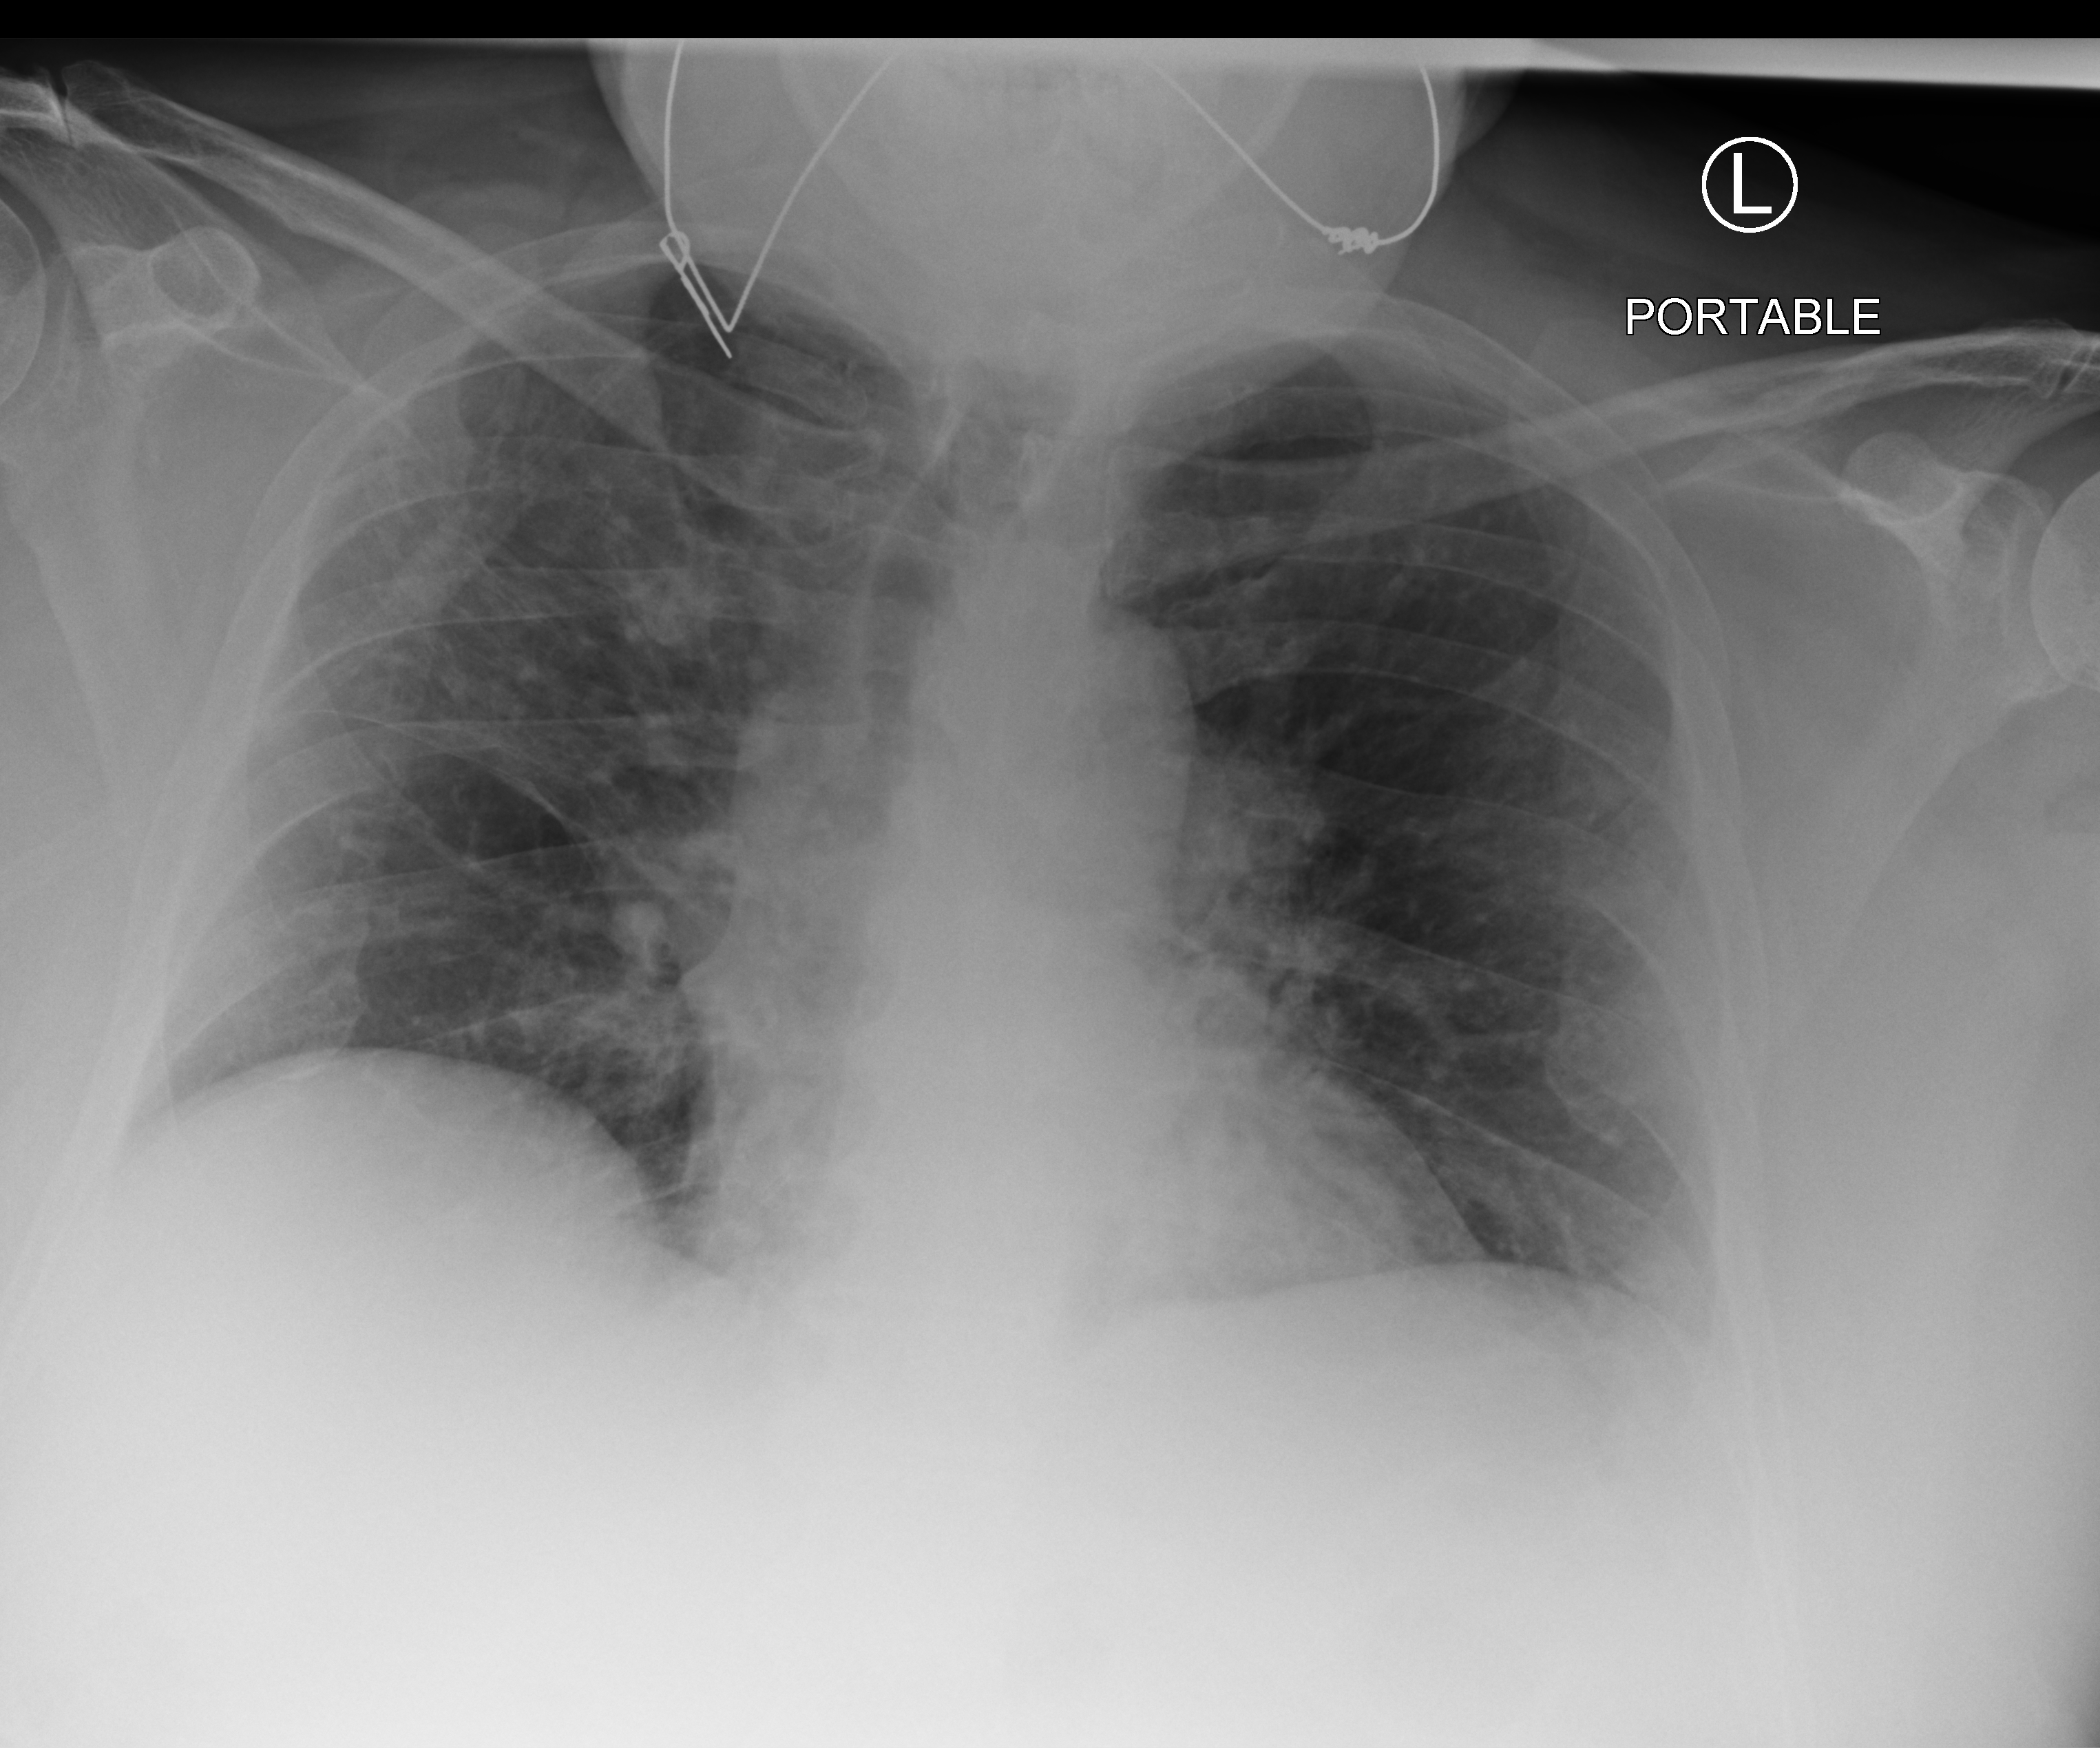
Bedside chest radiograph (computed radiography); anteroposterior (AP) projection. Patient hospitalised with COVID-19; male, aged 60–74 years.
From the hospital-stay record, not from the radiograph (when in the stay this image was taken is not recorded): diabetes (admission record): no; admitted to intensive care during this hospital stay: no.